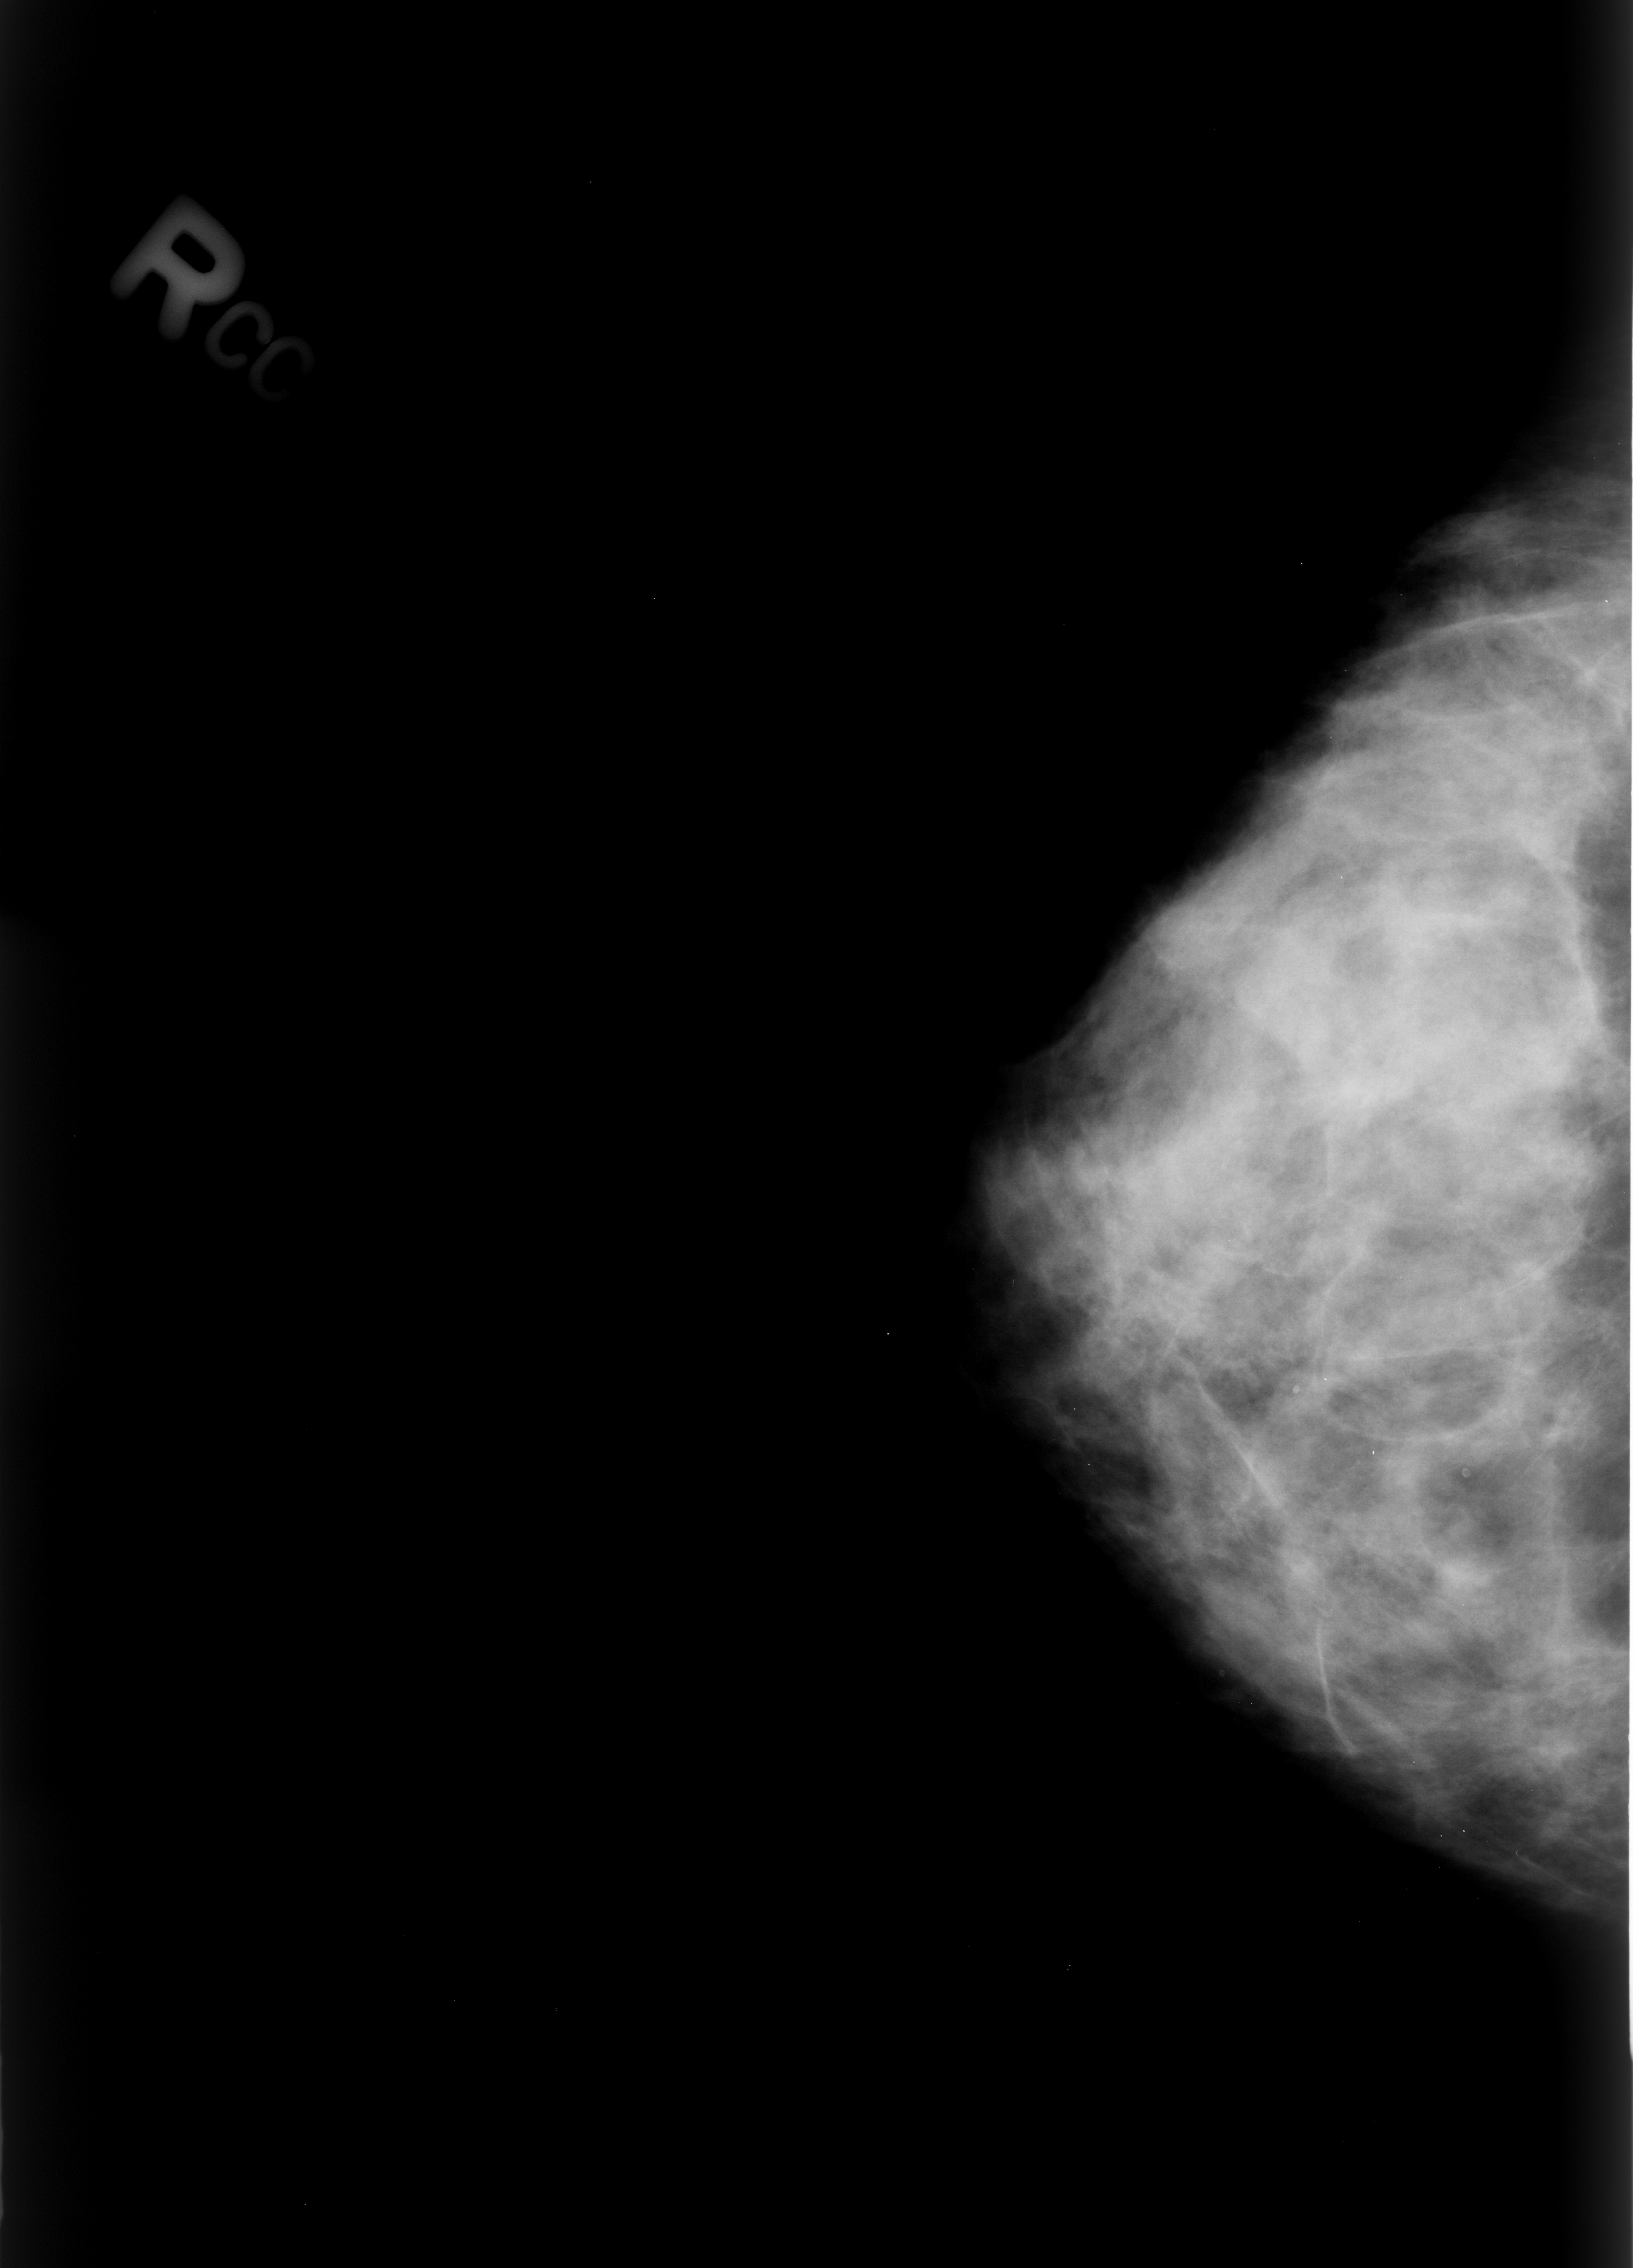
Digitized screen-film mammogram; right breast; craniocaudal (CC) view; breast composition: extremely dense (BI-RADS density category 4 of 4); 1633 × 2268 image matrix.
Expert-marked regions of interest on this film, with their recorded descriptors:
- Finding 1 of 2: calcifications, morphology lucent center; BI-RADS assessment category 2; subtlety rating 4 on a 1 (subtle) to 5 (obvious) scale; benign; no additional work-up was recommended (outcome (as recorded, no biopsy): benign without callback): box from (x=1260, y=1359) to (x=1355, y=1450) px
- Finding 2 of 2: calcifications, morphology lucent center; BI-RADS assessment category 2; subtlety rating 4 on a 1 (subtle) to 5 (obvious) scale; benign; no additional work-up was recommended (outcome (as recorded, no biopsy): benign without callback): (x=1435, y=1449)–(x=1514, y=1510)